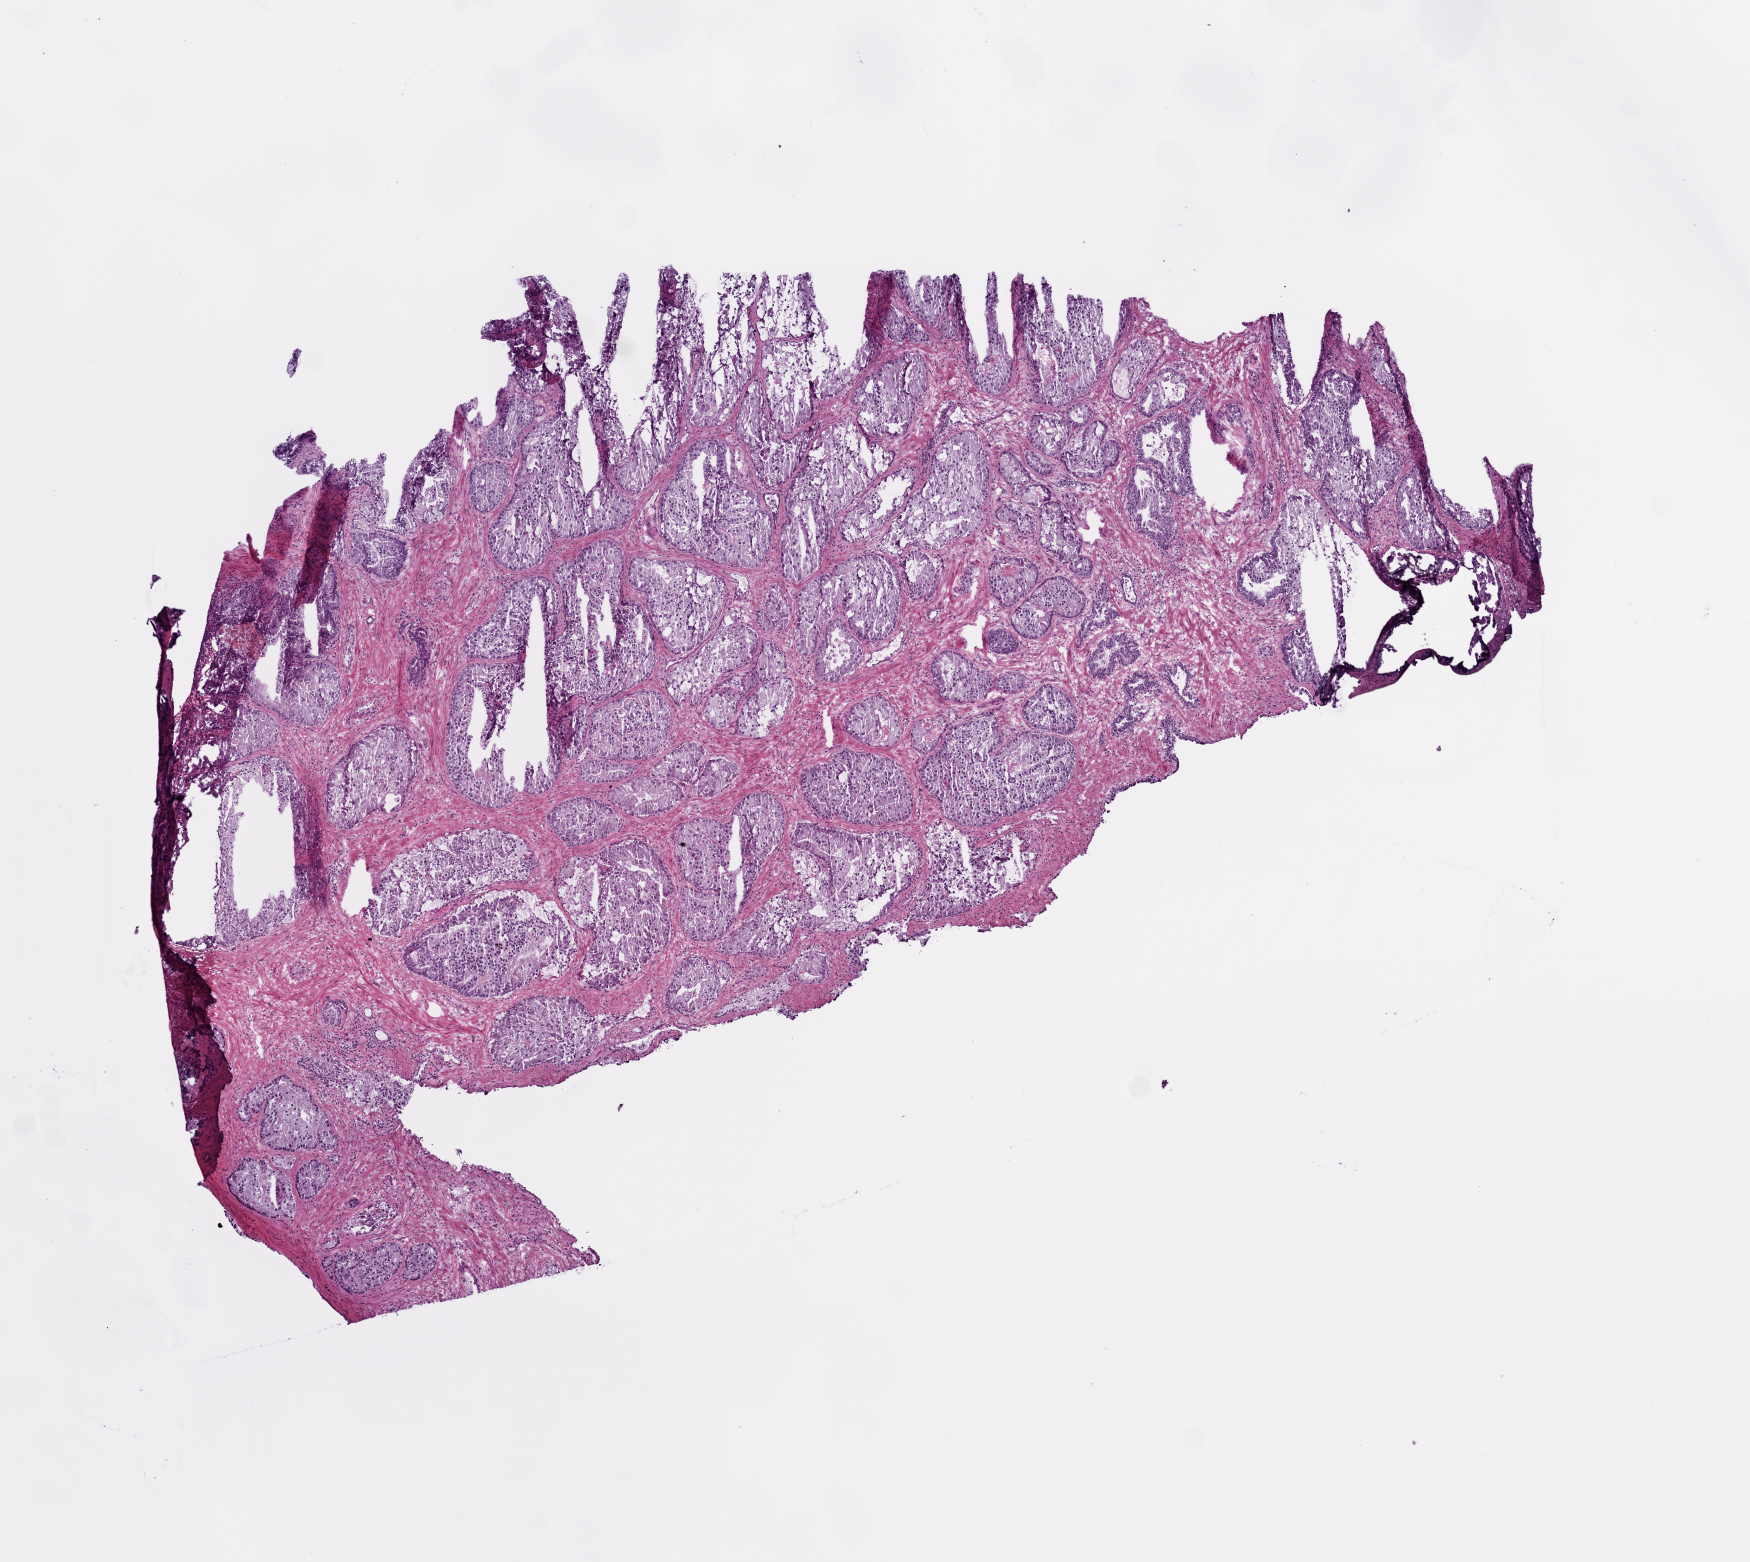
Digitized Hematoxylin and eosin (H&E) stained tissue section (whole slide) — a low-resolution overview of the entire scanned area, about 7.0 x 6.3 mm (acquisition: 20x scan). Frozen section from the bottom of the tissue portion. Prostate, primary tumour sample. Patient: male, age at initial diagnosis 63 years. Gleason score: 7 (3+4). Pathologist review of this section (percent, as recorded): tumour cells 55%, tumour nuclei 55%, normal cells 15%, stromal cells 28%, necrosis 2%. Inflammatory infiltration, as recorded: lymphocyte infiltration 4%, monocyte infiltration 2%, neutrophil infiltration 0%.
- diagnosis: Acinar cell carcinoma (prostate gland)
- lymph nodes positive (case pathology): 0 of 2 examined